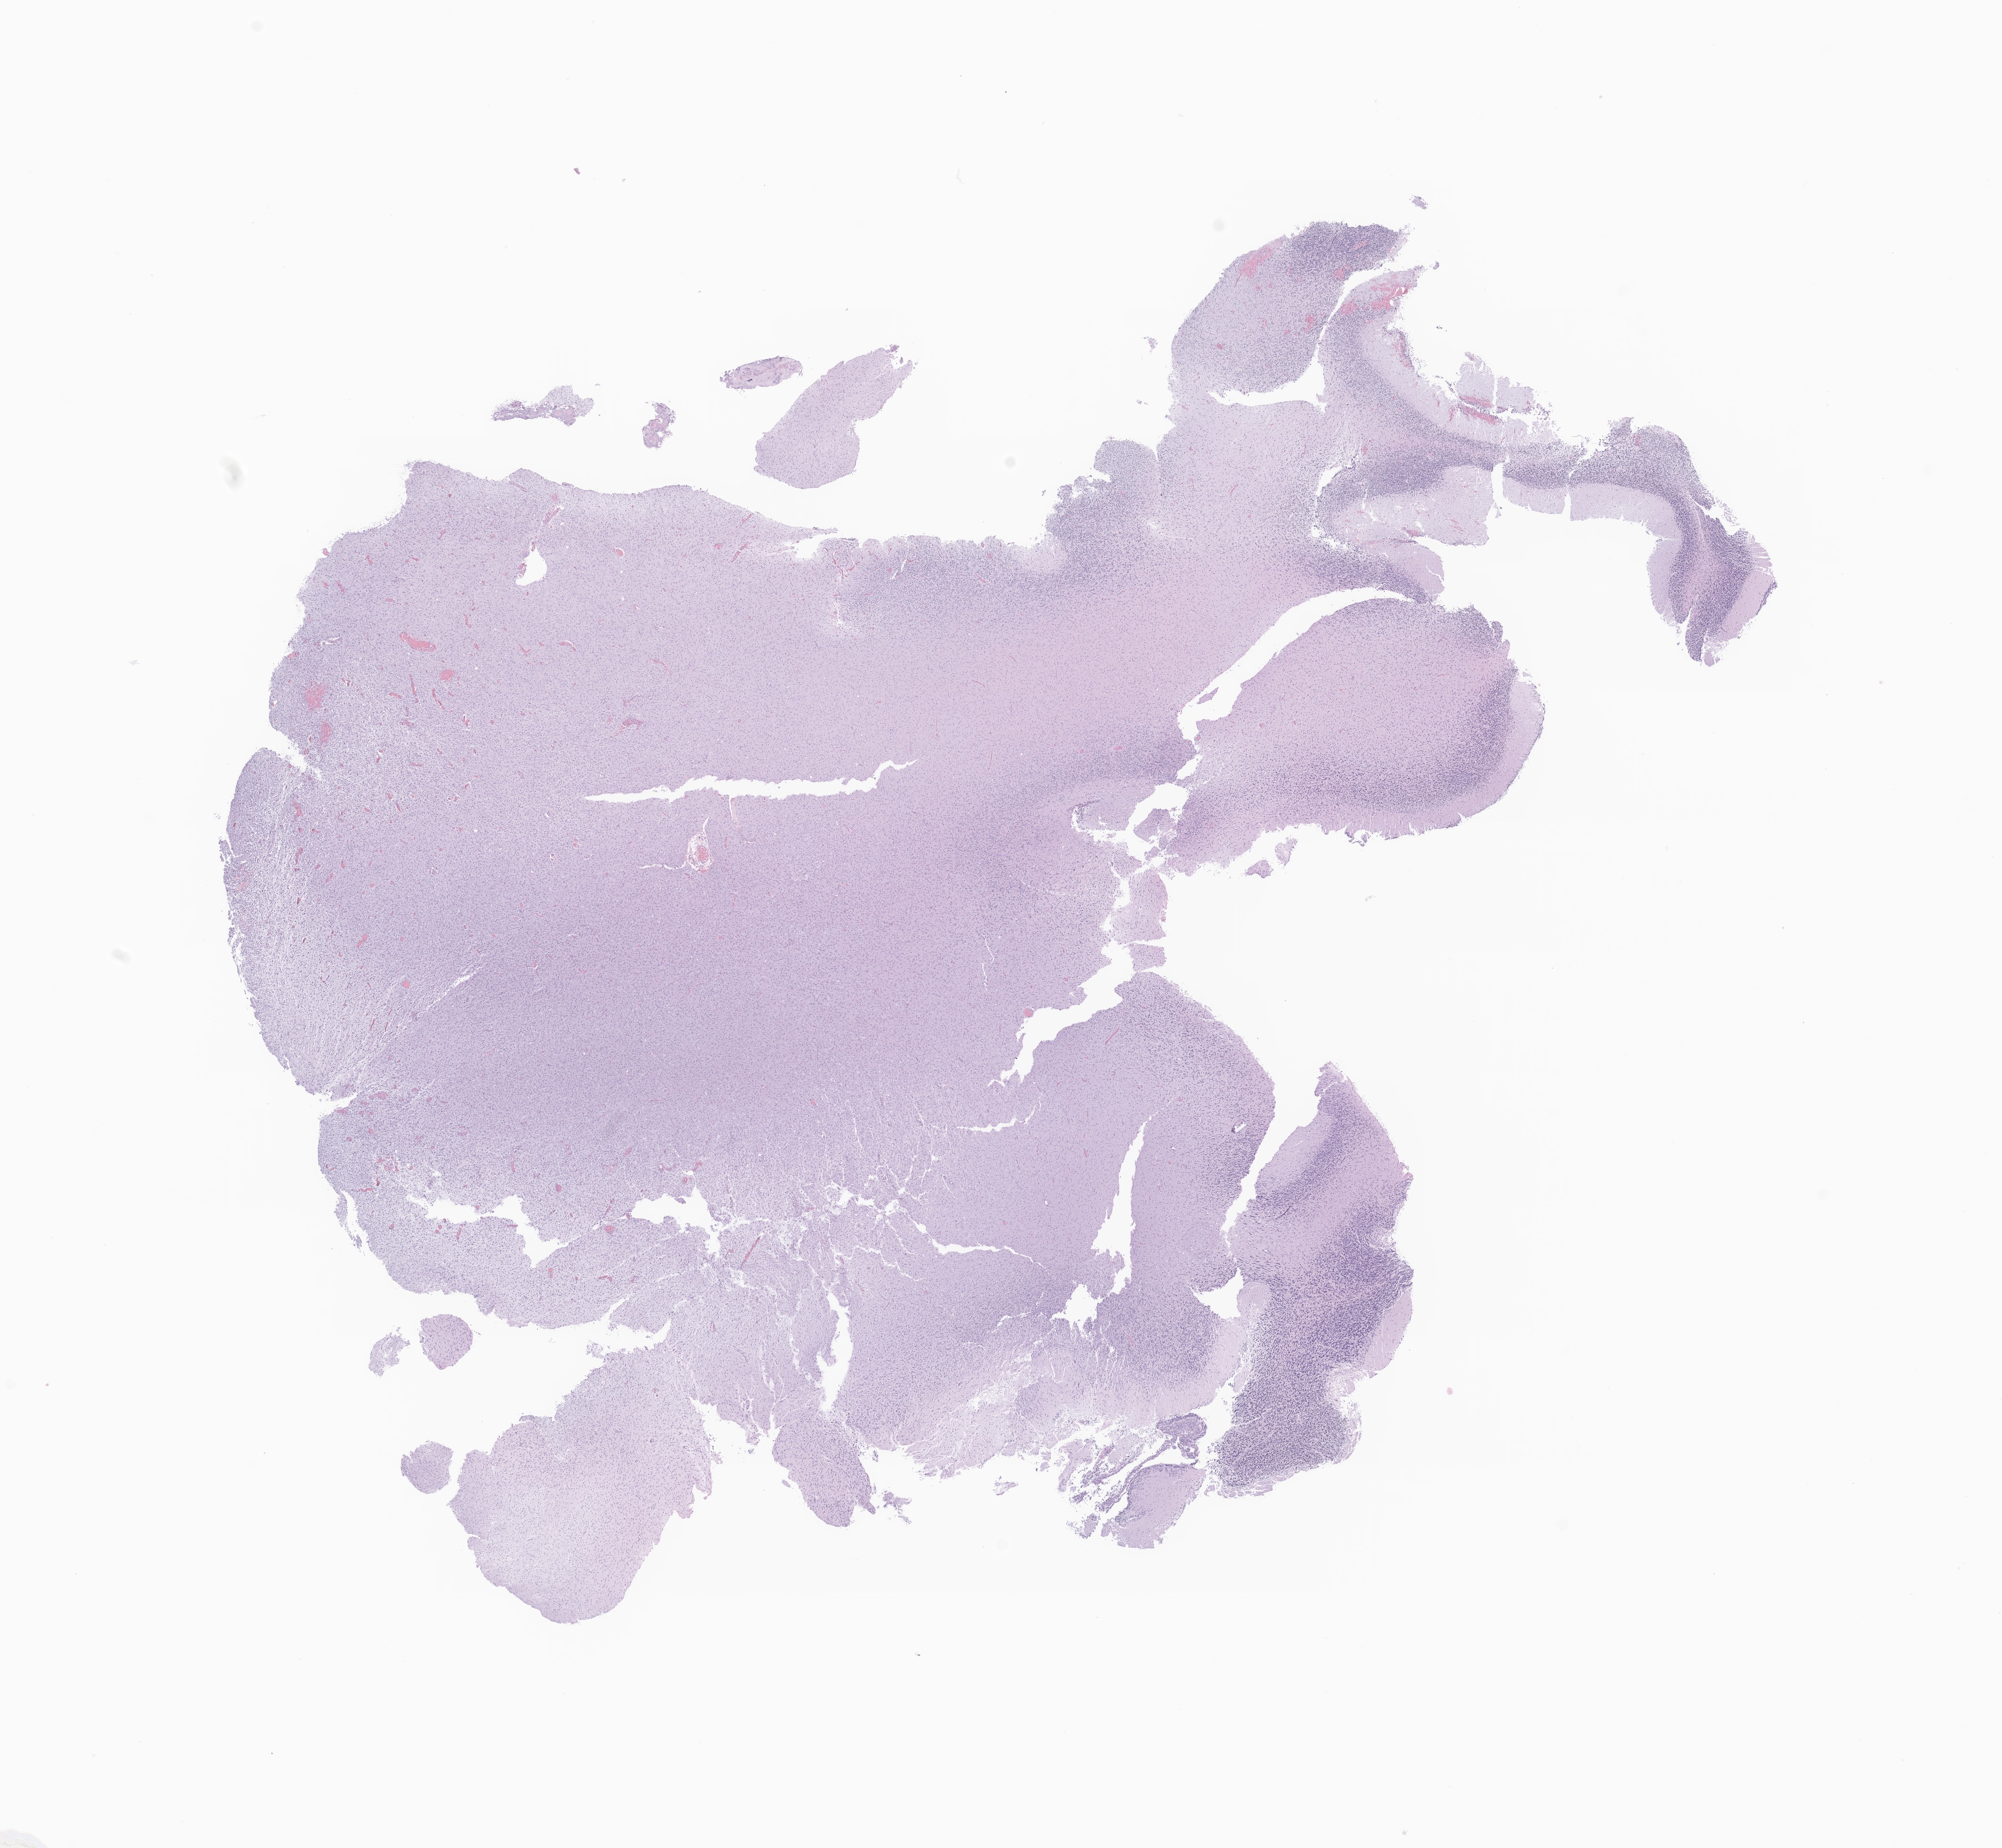
Hematoxylin and eosin (H&E) whole-slide image of tumor tissue from the brain — shown as a low-resolution overview of the whole scanned area (about 16.6 x 15.4 mm); FFPE section. Patient female; age 453 days (about 1.2 years).
Recorded diagnosis: Pilocytic astrocytoma.